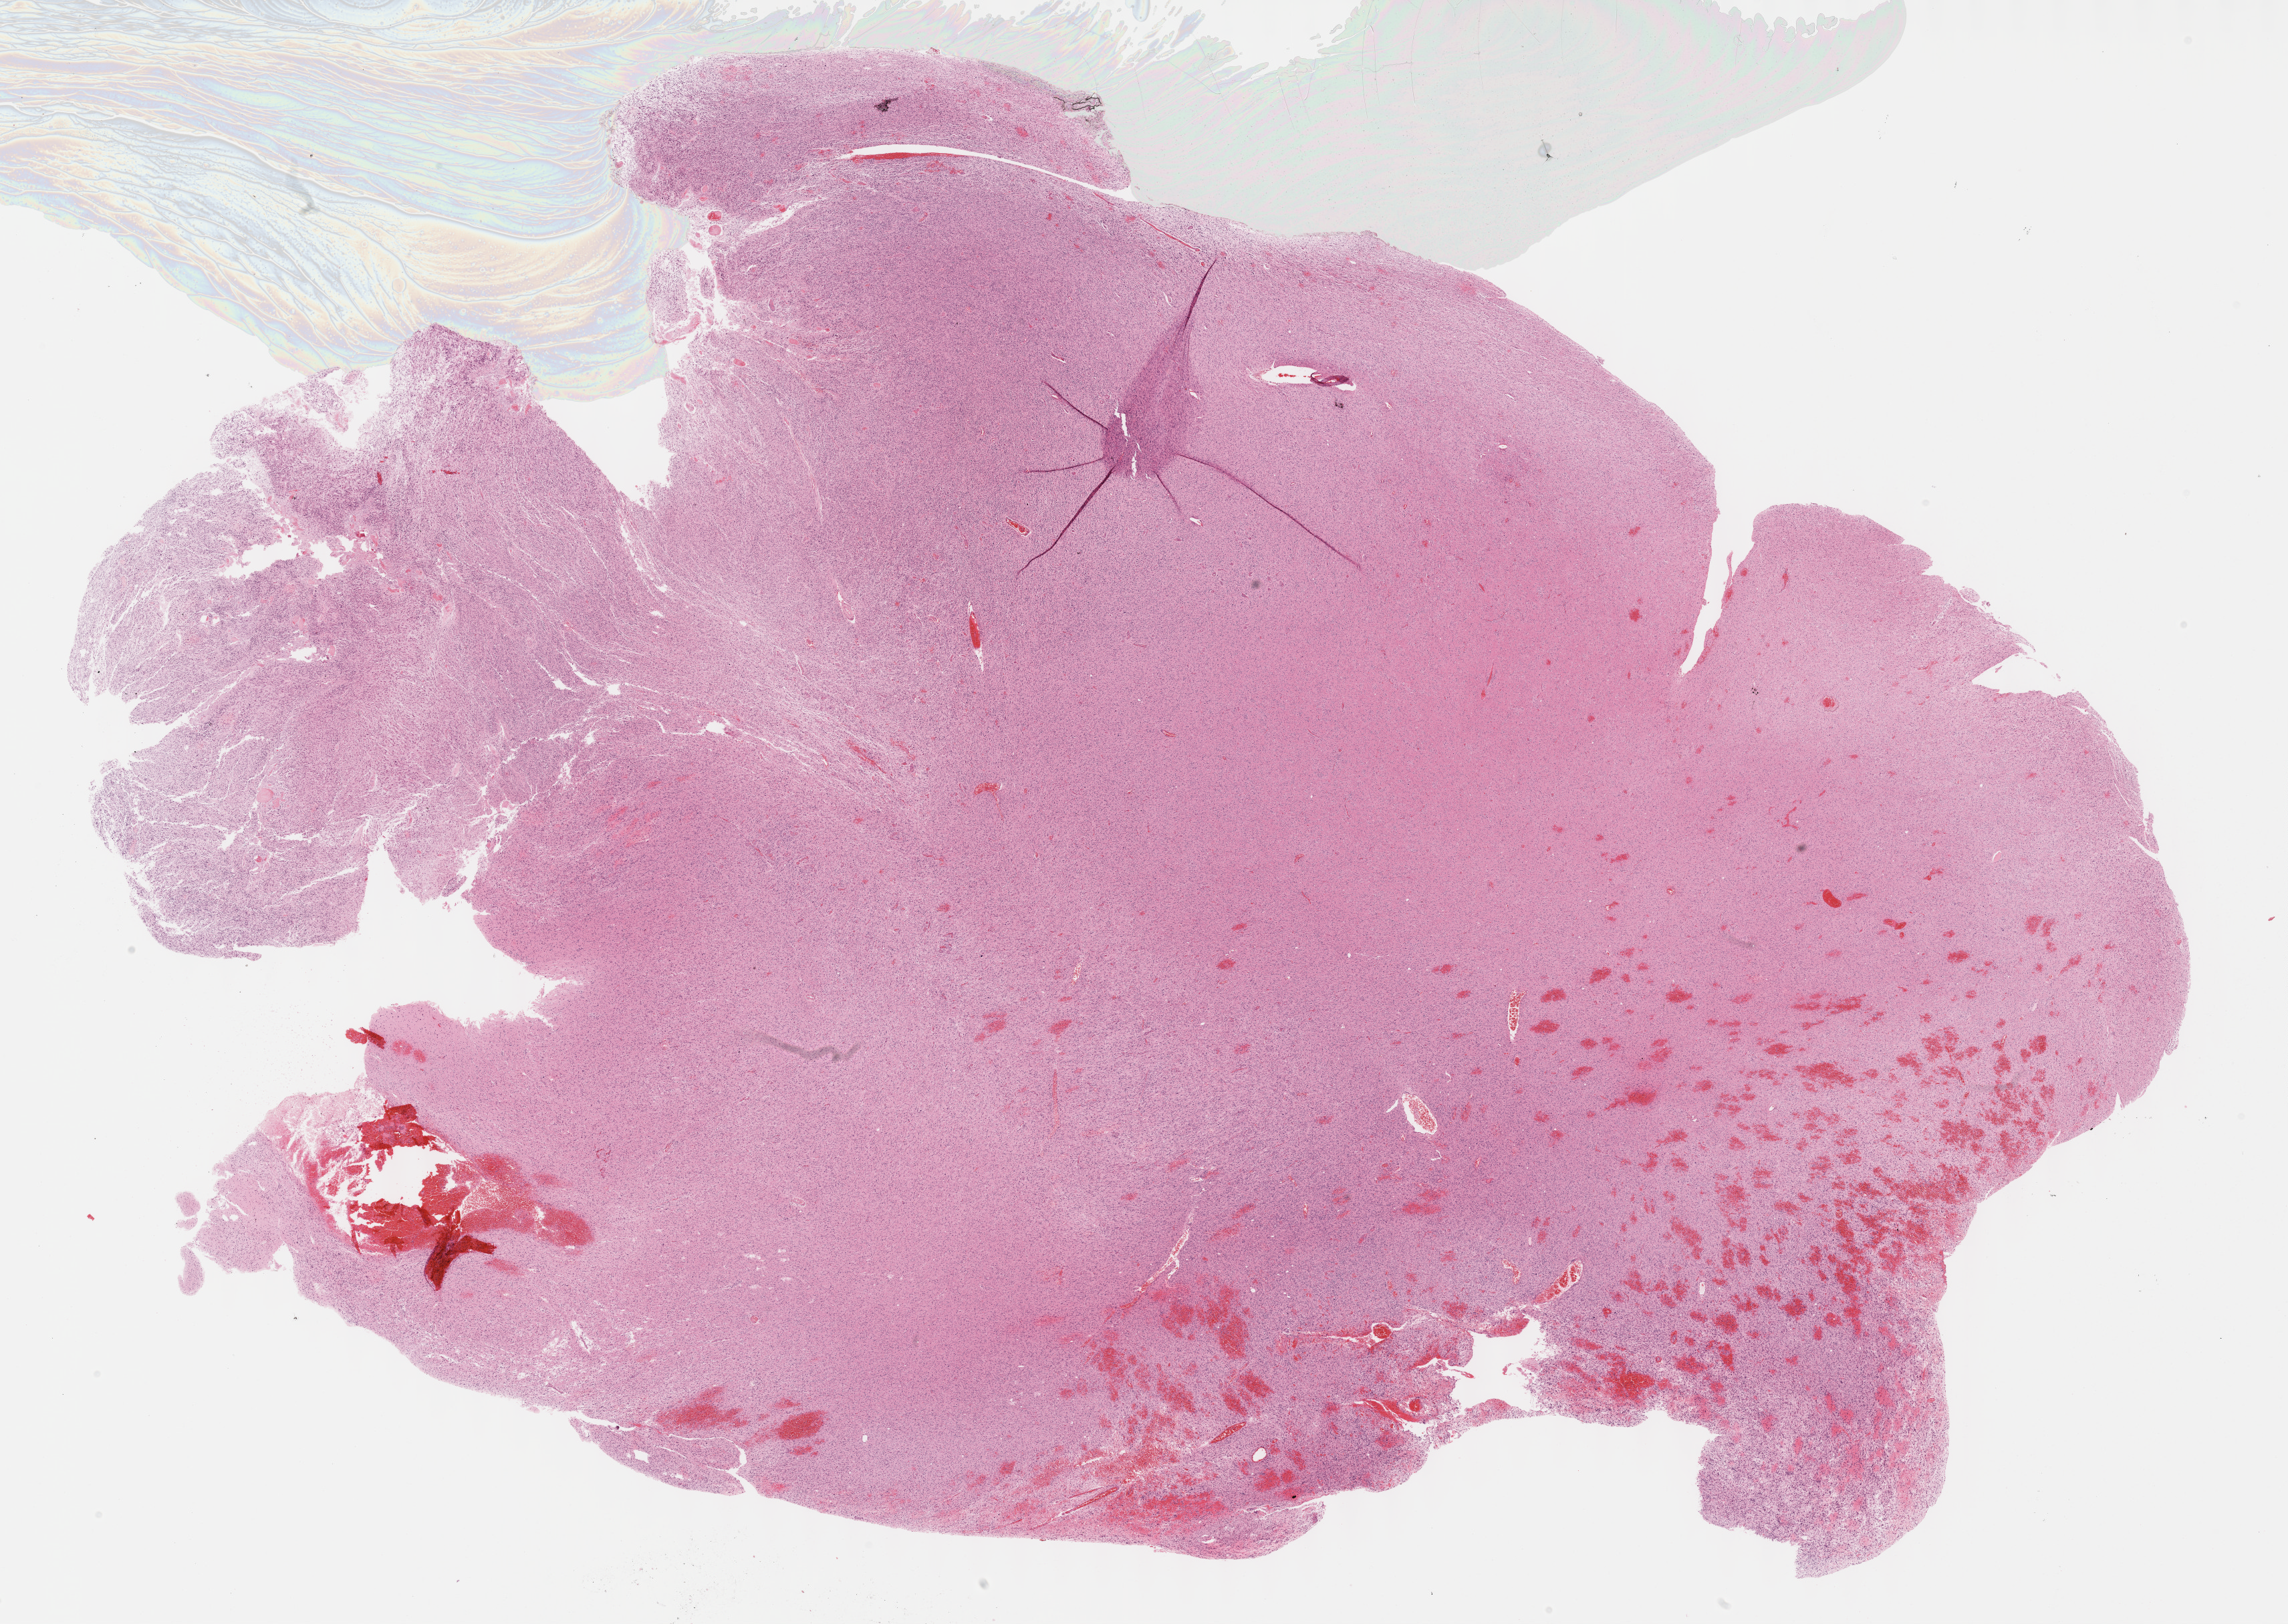
Digitized H&E tissue section (whole slide) — low-resolution overview of the scanned area, about 27.7 x 19.6 mm (acquisition: 40x scan). FFPE section. Primary tumour sample from the brain. Female, age 59 years at initial diagnosis.
Diagnosis: Glioblastoma.